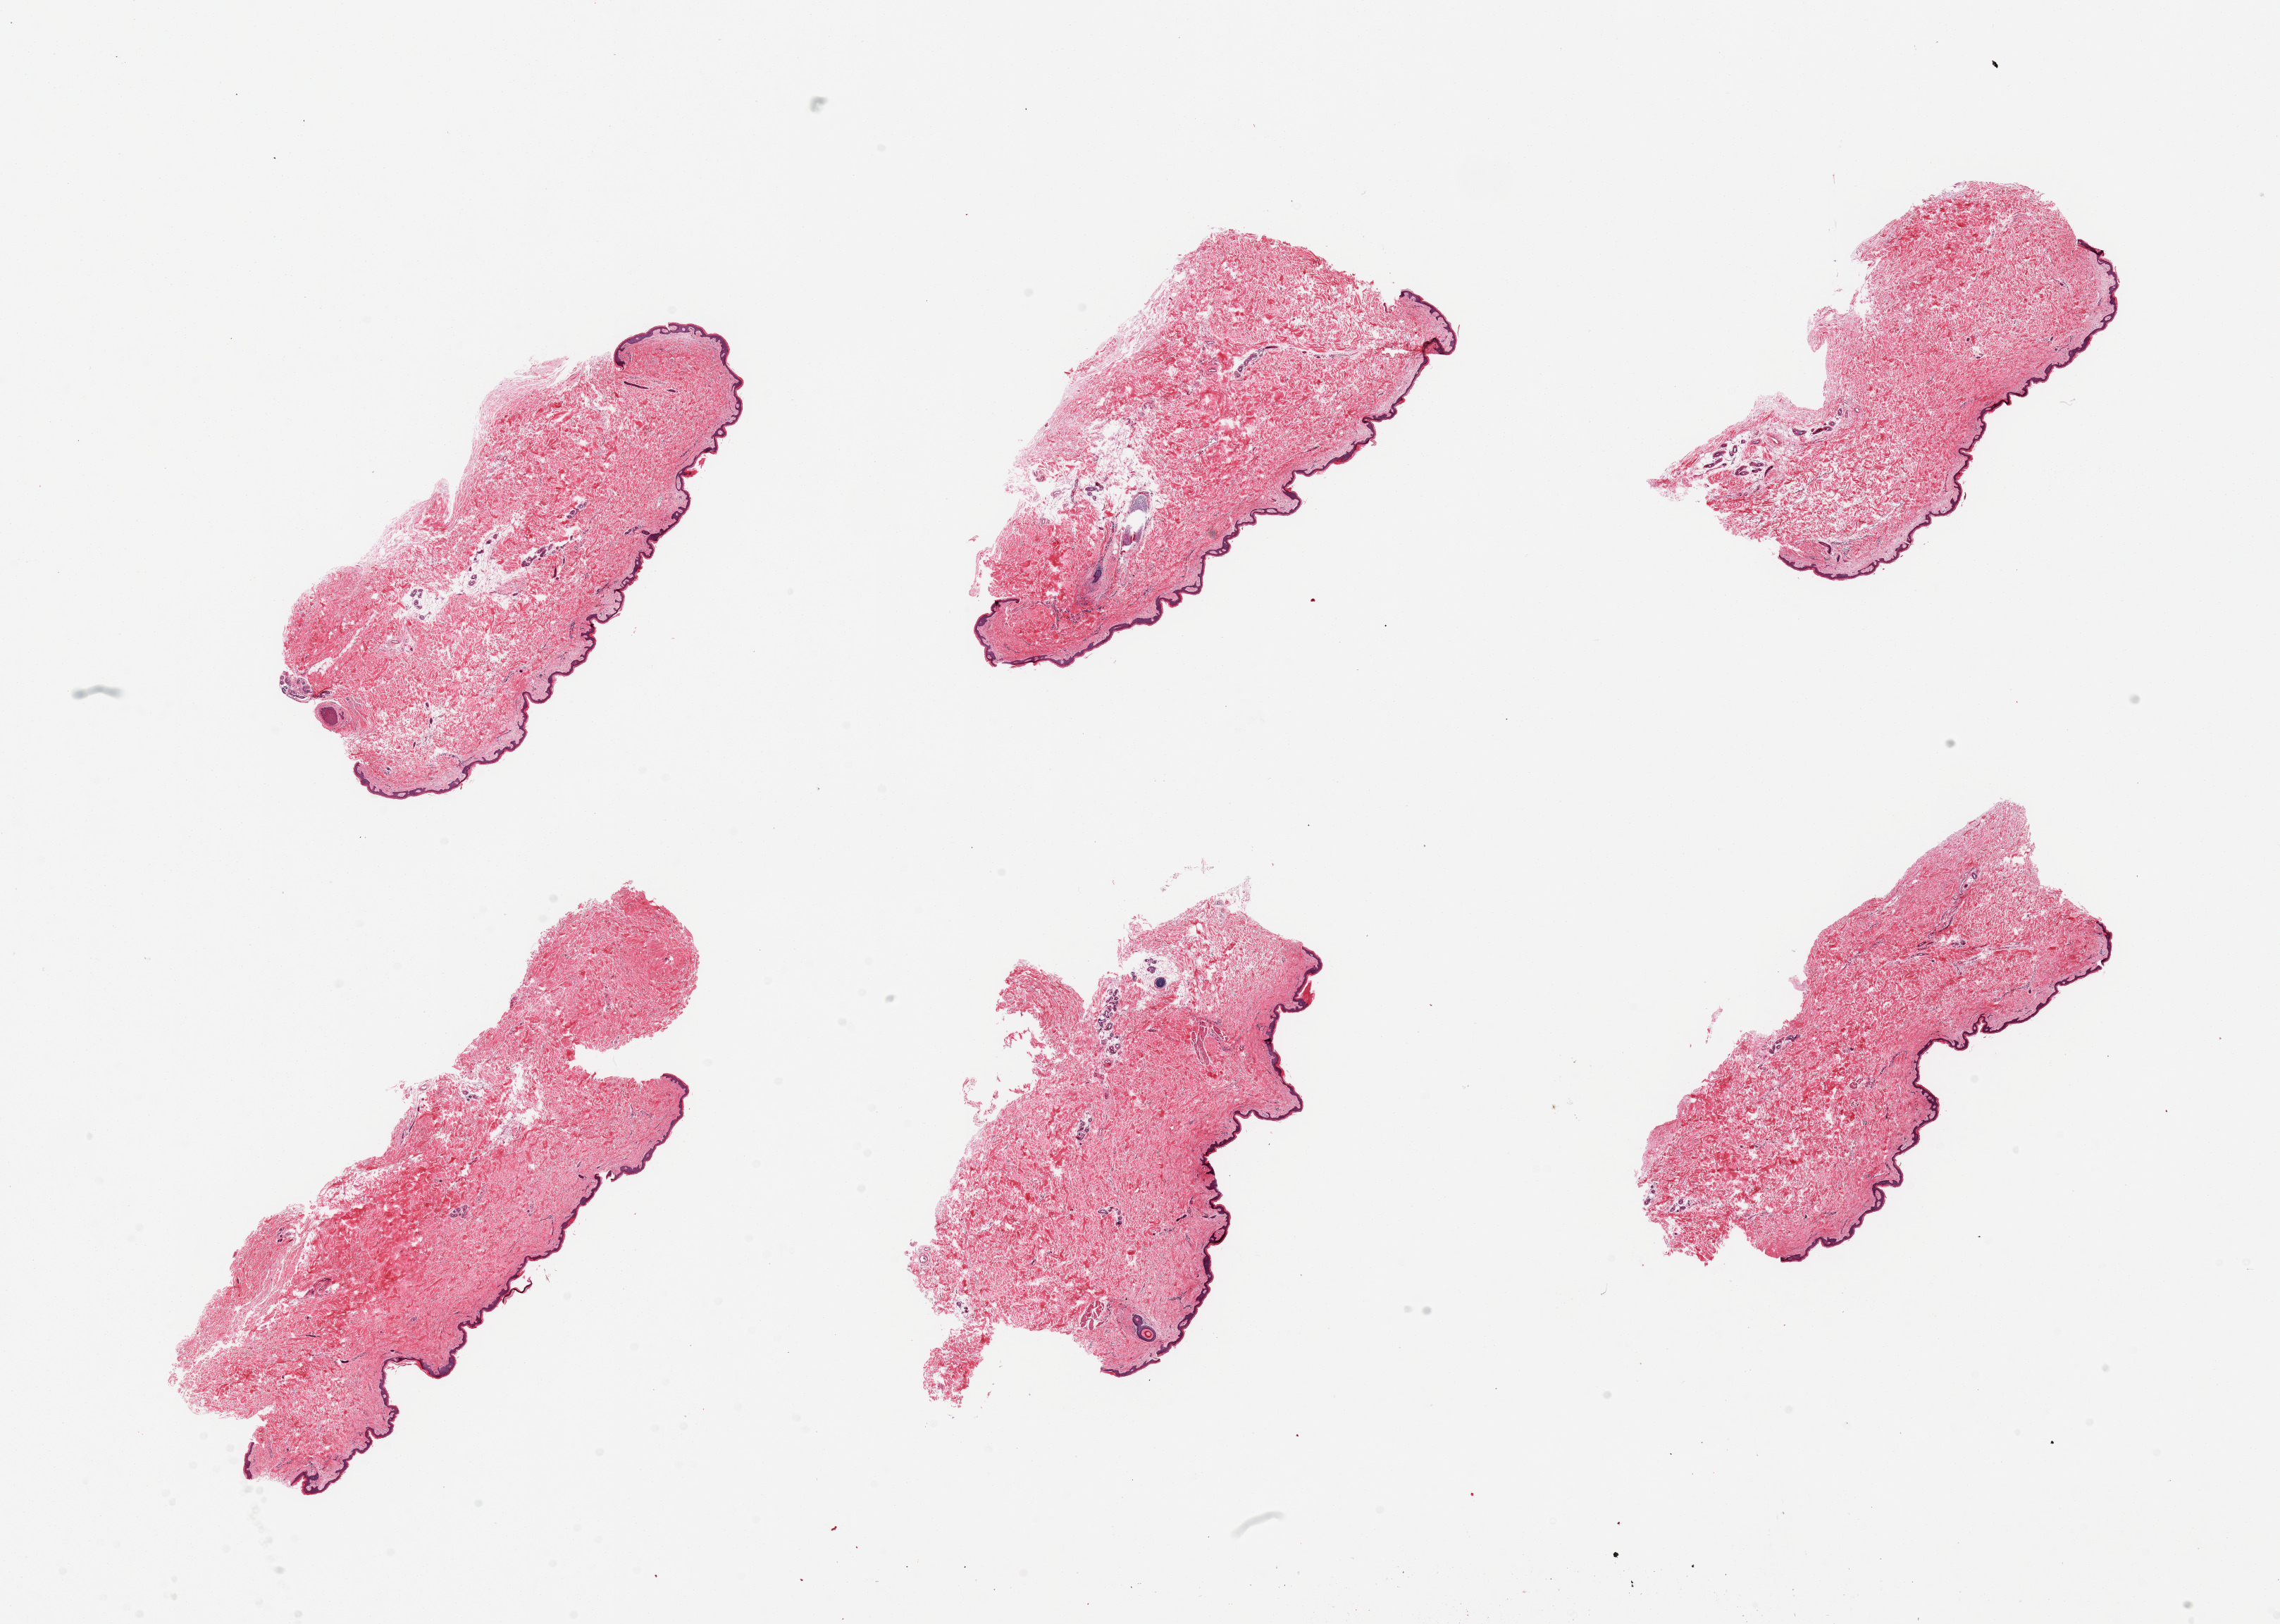
Whole-slide image, hematoxylin and eosin (H&E) stain — low-resolution overview of the scanned area, about 25.6 x 18.2 mm (from a 20x scan). PAXgene-fixed, paraffin-embedded tissue. Sampled site (target tissue): skin of suprapubic region. Tissue donor sample. Donor: female.
Pathologist's review note for this sample: 6 pieces; ~5% - 10% periadnexal fat.